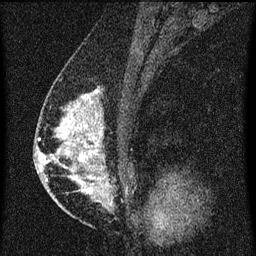
Breast MRI (dynamic contrast-enhanced), one sagittal slice; dynamic contrast-enhanced series, image 2 of 3 at this slice position (ordered by acquisition); 1.5 T; TE 4.2 ms, TR 8 ms; 2 mm slice thickness; 256 × 256 image matrix, field of view 180 × 180 mm. Female patient, age 47 years.
Annotated regions visible in this slice (semi-automatic segmentation, software-assisted and operator-edited):
- analysis volume of interest (the breast-tissue region the enhancement analysis was run in; not a lesion): bounding box <50,80,131,203> (left, top, right, bottom; pixels)
- tumour enhancement mask (voxels above the 70 % enhancement threshold inside the analysis volume of interest): <50,92,104,195>